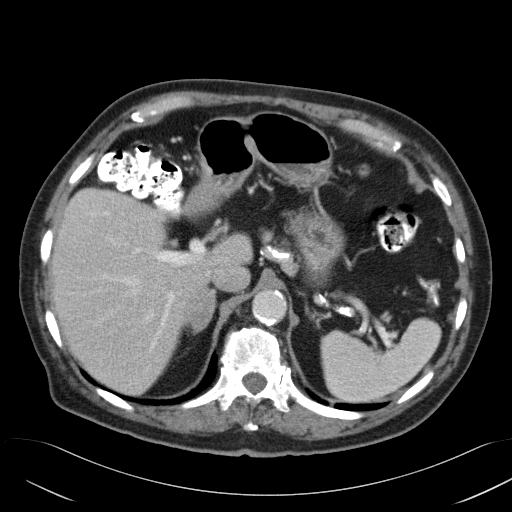
Contrast-enhanced abdominal CT, one axial slice; position 36 of 58 along the scan axis; reconstruction kernel B31f; 120 kVp; intravenous contrast given; soft-tissue window (W 400 / L 40 HU); 512 × 512 image matrix, field of view 384 × 384 mm. Patient: male, 82 years. From the clinical record (not read from this slice): diagnosis: adrenocortical carcinoma; tumour side: right adrenal; tumour size at pathology: 9 cm; Ki-67 index: 30 %; stage (as recorded): 3.
Outlined on this slice (semi-automatically segmented with operator editing):
- mass: bounding box (x1, y1, x2, y2) in pixels: (188, 291, 216, 326)